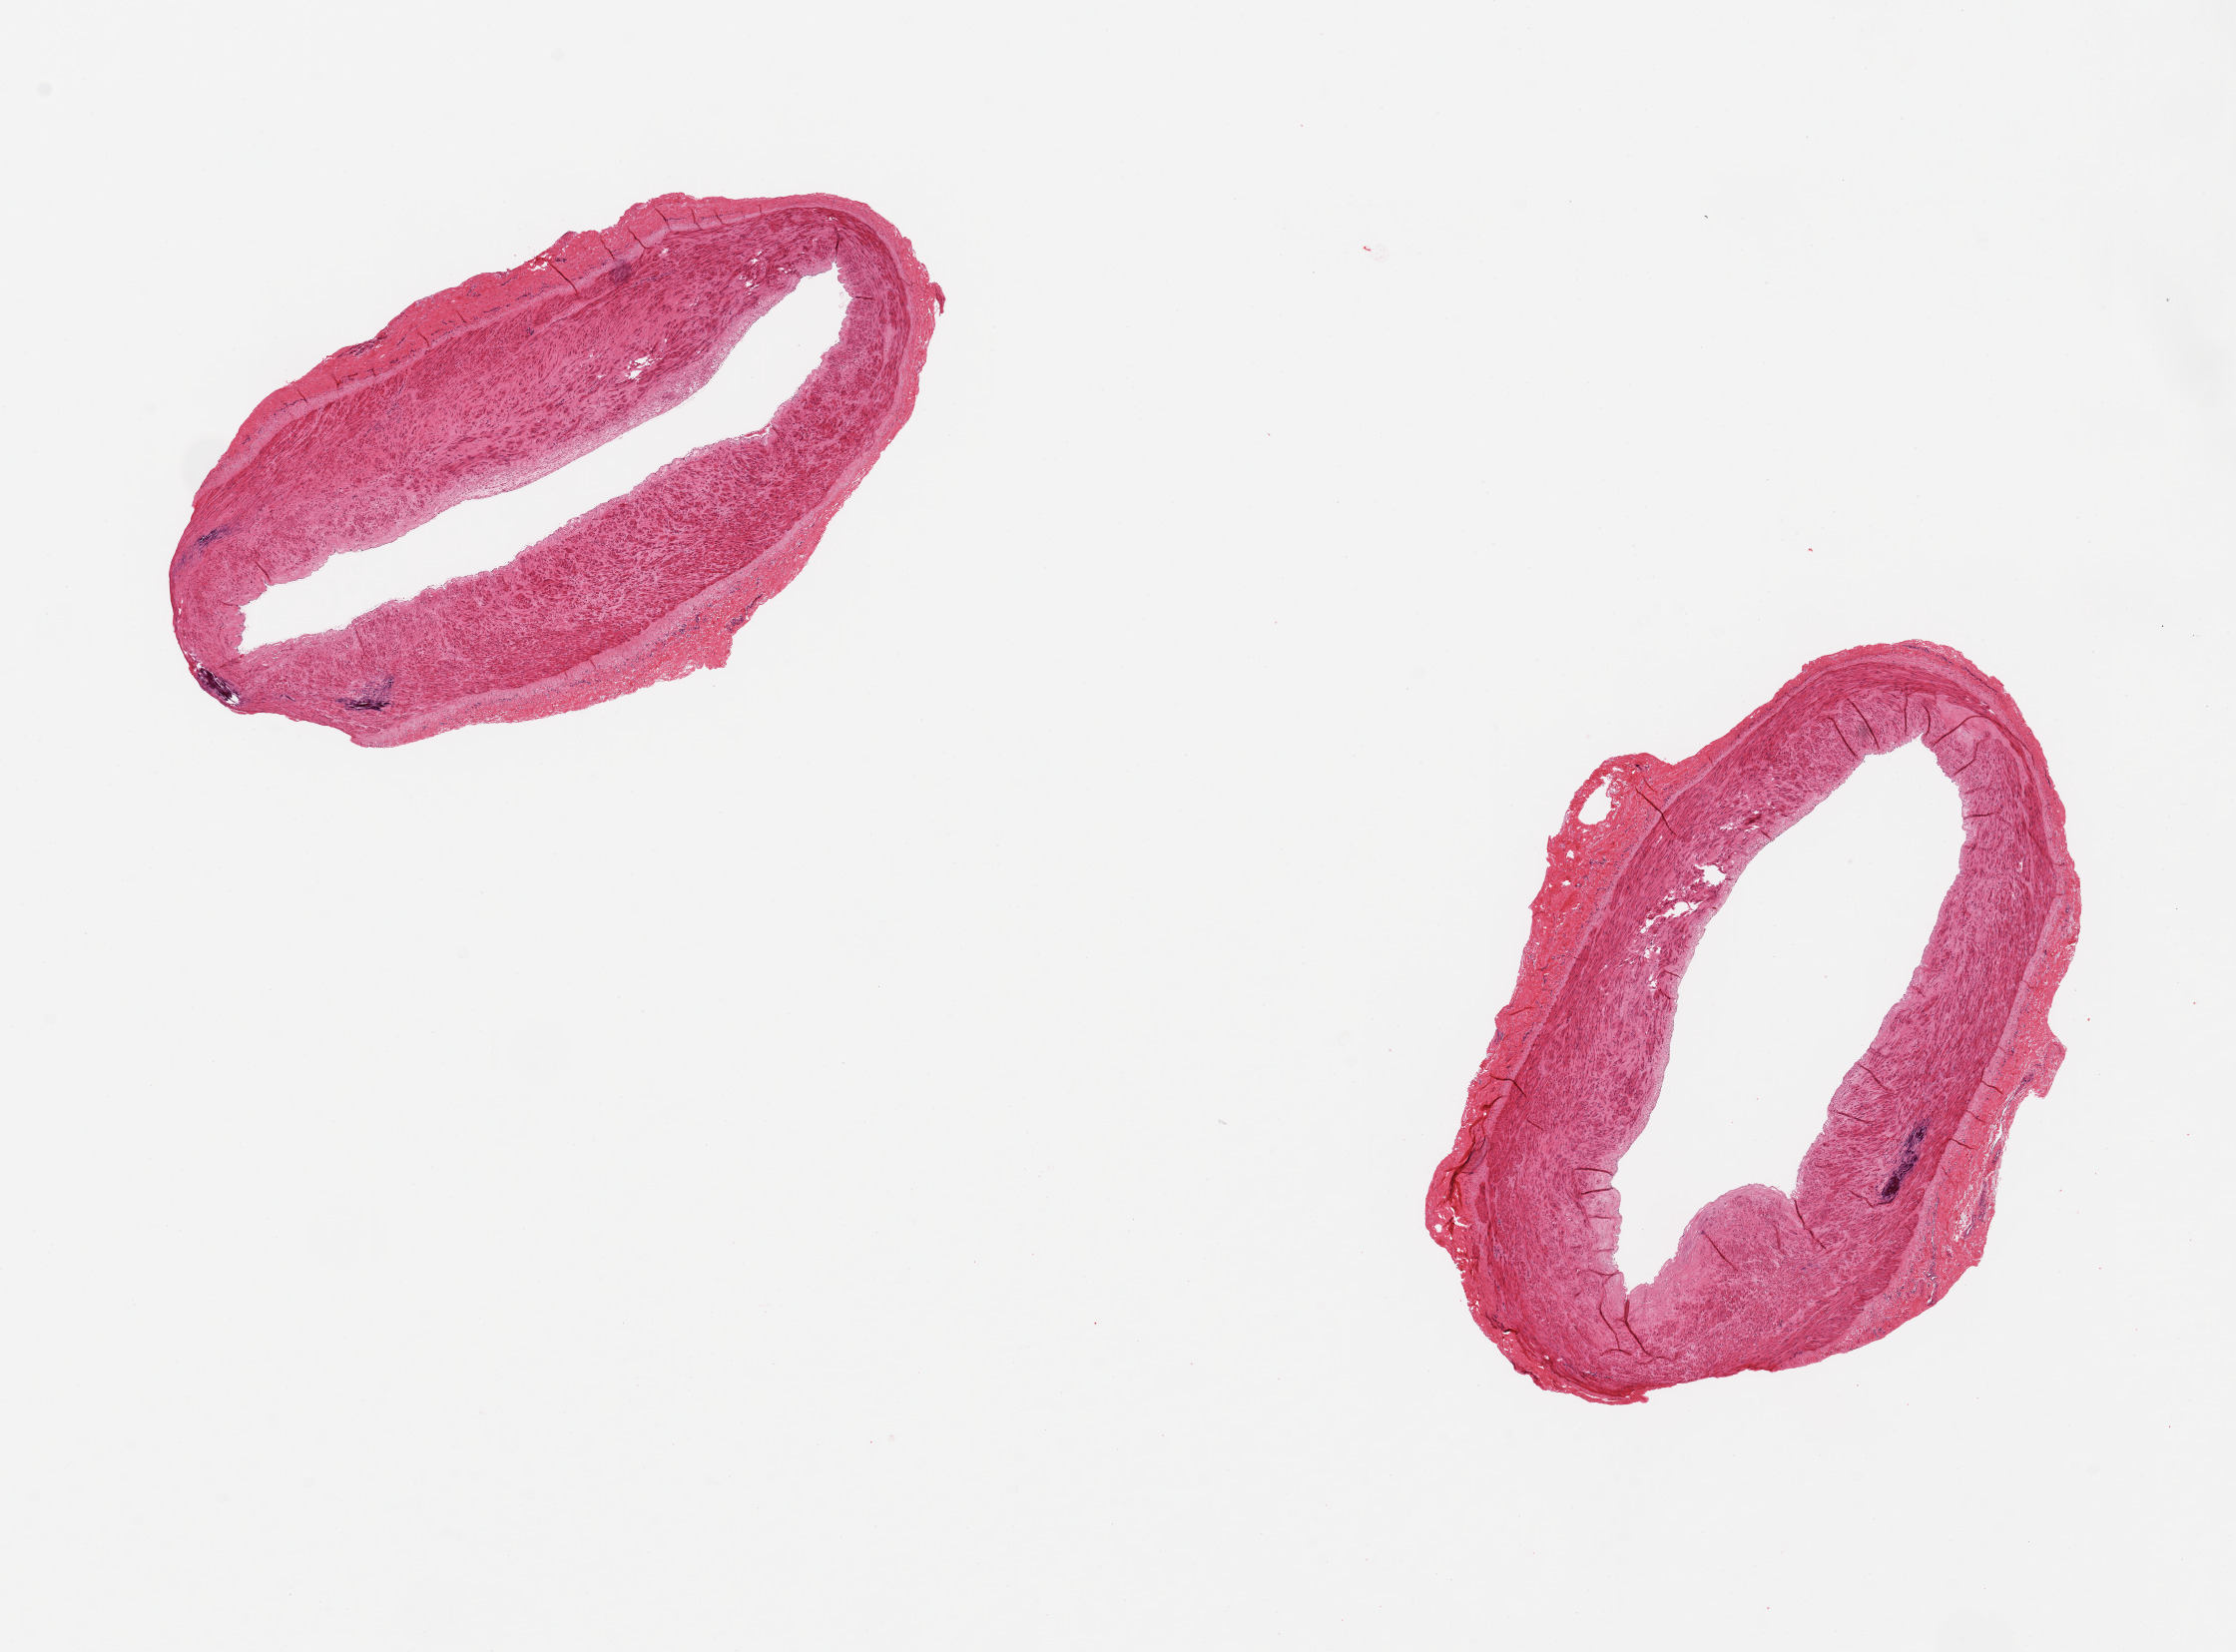
Digitized hematoxylin and eosin (H&E)-stained section, brightfield, shown as a low-resolution overview of the whole scanned area (about 17.7 x 13.1 mm, slide scanned at 20x), PAXgene-fixed paraffin-embedded (PFPE) section, sampled site (target tissue): tibial artery, tissue donor sample. Donor: male.
Review note (as recorded): 2 pieces ~5mm d; Foci of Monckeberg medial sclerosis.